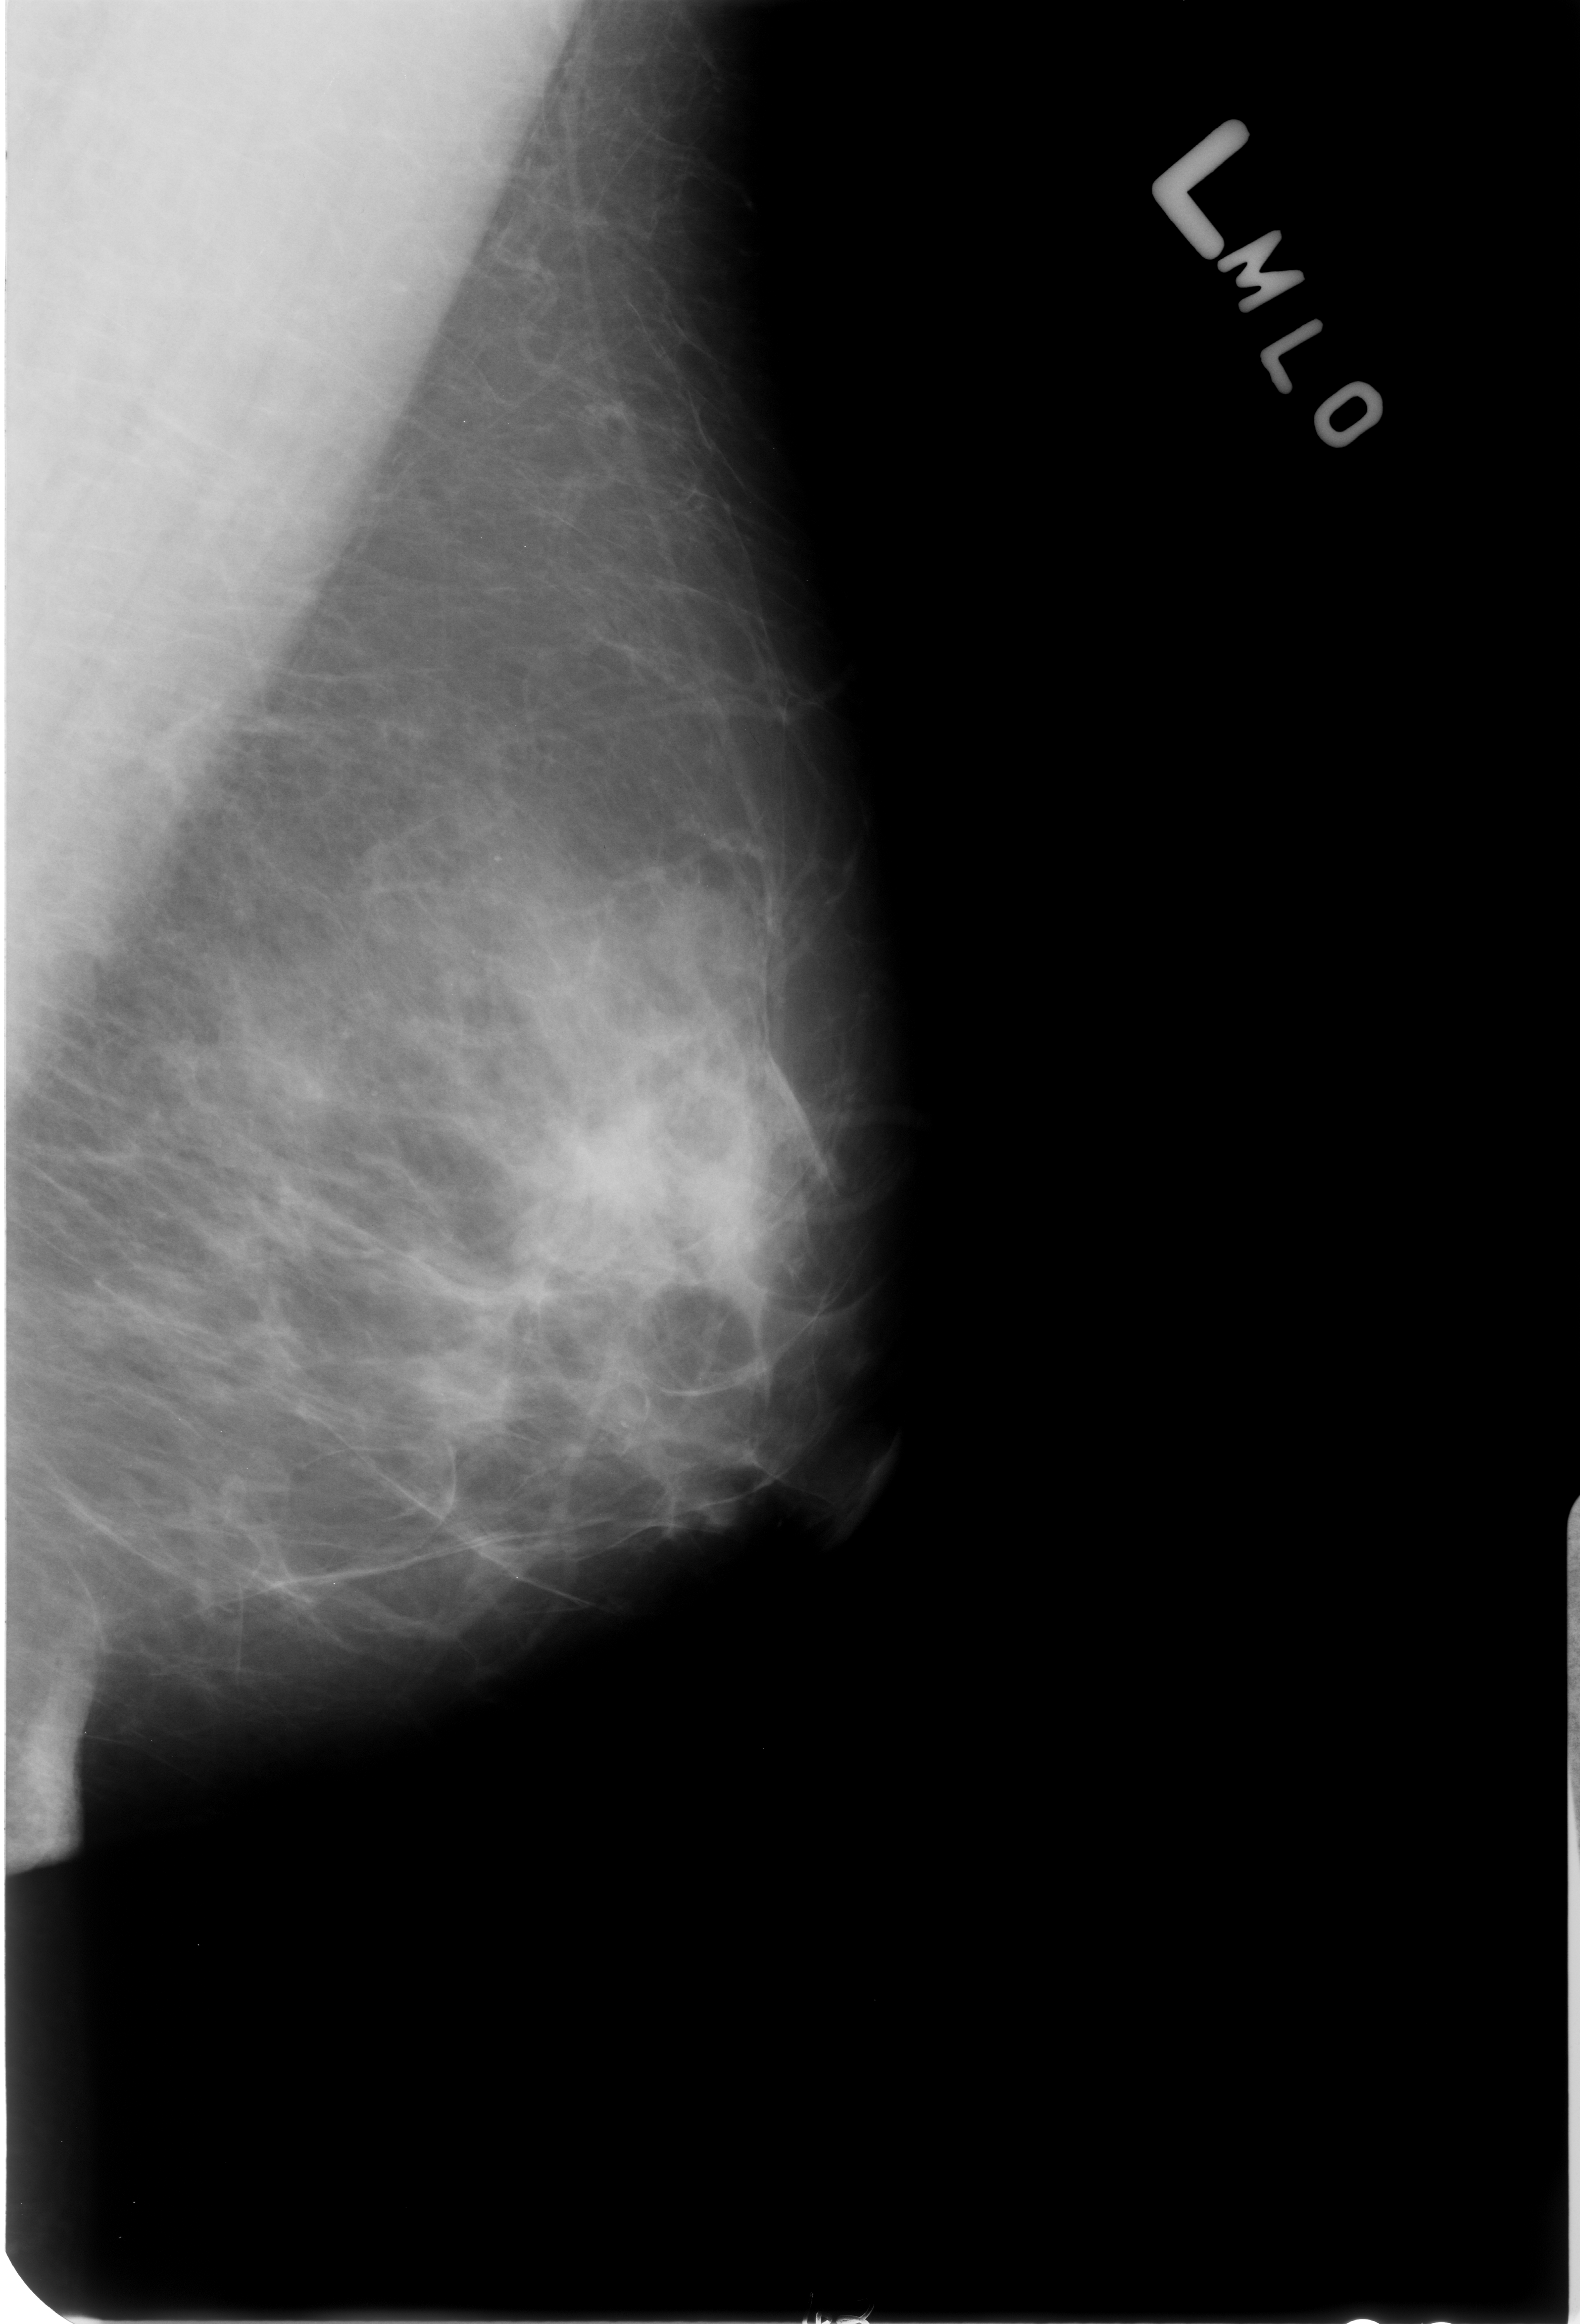
Mammogram (digitized film). Left breast. MLO view. BI-RADS breast density category 3 (scale 1–4). 1580 × 2324 image matrix.
Expert-marked regions of interest on this film, with their recorded descriptors:
- calcifications, morphology punctate, distribution segmental; BI-RADS assessment category 2; subtlety rating 3 on a 1 (subtle) to 5 (obvious) scale; benign; no additional work-up was recommended (outcome (as recorded, no biopsy): benign without callback): bounding box [x1, y1, x2, y2] px = [416, 763, 579, 894]